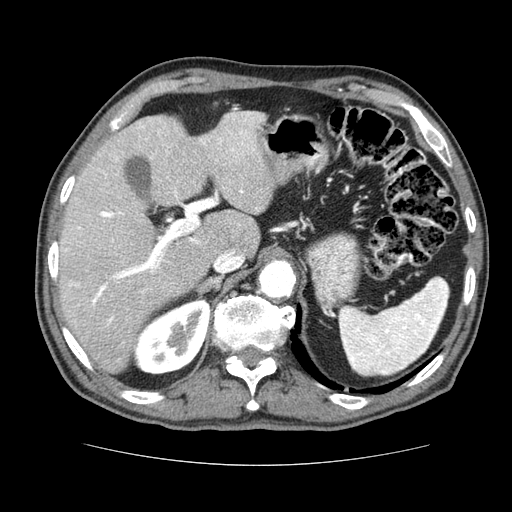
Contrast-enhanced abdominal CT (liver protocol), one axial slice; slice 48 of 79 in the series (ordered by position); 120 kVp; soft-tissue window (W 400 / L 40 HU); 2.5 mm slice thickness; 512 × 512 image matrix. Case-level facts recorded for this patient, not image findings: diagnosis: hepatocellular carcinoma (patient treated with transarterial chemoembolisation; whether this scan precedes or follows treatment is not stated here); TNM stage (as recorded): Stage-I; Child-Pugh class: A; tumour nodularity: uninodular.
Outlined on this slice (semi-automatic segmentation, software-assisted and operator-edited):
- liver parenchyma outside the tumour (the mass and vessels are separate outlines, so this box may not span the whole liver): bounding box <58,112,274,372> (left, top, right, bottom; pixels)
- liver vessels: <64,112,261,325>